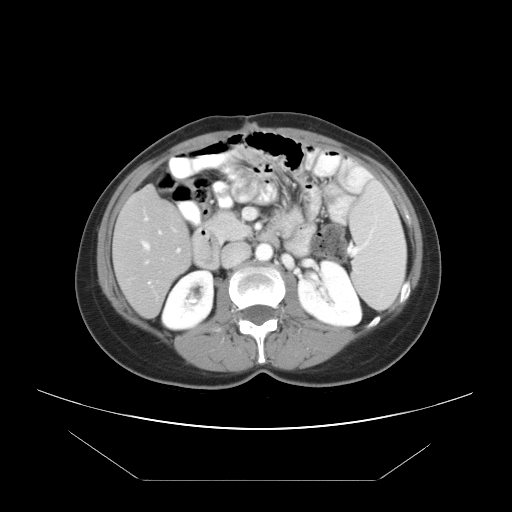
Contrast-enhanced abdominal CT, one axial slice. Position 17 of 45 along the scan axis. Reconstruction kernel STANDARD. 120 kVp. Intravenous contrast given. Soft-tissue window (W 400 / L 40 HU). 5 mm slice thickness. 512 × 512 image matrix, field of view 405 × 405 mm. Female patient, age 52 years. Case-level facts recorded for this patient, not image findings: diagnosis: colorectal cancer liver metastases, imaged before liver resection; multiple liver metastases: yes; largest metastasis: 2.5 cm; disease in both lobes: no.
Annotated regions visible in this slice (manually delineated by an expert):
- hepatic veins: box from (x=143, y=231) to (x=161, y=284) px
- liver: (x=115, y=189)–(x=190, y=316)
- planned liver remnant (the part of the liver to remain after resection): (x=116, y=189)–(x=190, y=253)
- portal vein (with intrahepatic branches): (x=144, y=216)–(x=181, y=264)